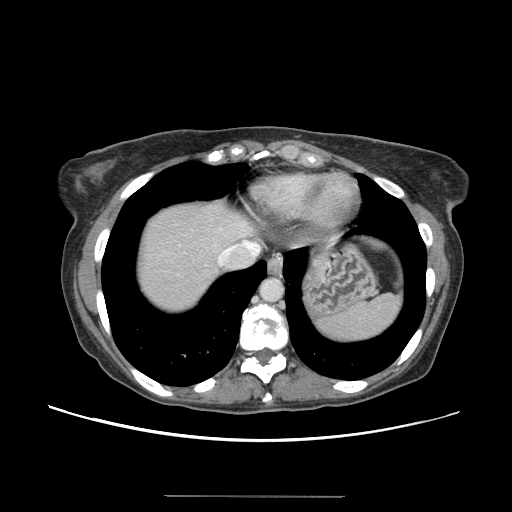
Contrast-enhanced abdominal CT, one axial slice. Position 129 of 144 along the scan axis. 120 kVp. Intravenous contrast given. Soft-tissue window (W 400 / L 40 HU). 512 × 512 image matrix. Female patient, age 53 years. From the clinical record (not read from this slice): diagnosis: colorectal cancer liver metastases, imaged before liver resection; multiple liver metastases: yes; largest metastasis: 1.1 cm; disease in both lobes: no.
Structures marked on this image (expert manual segmentation):
- hepatic veins: bounding box [x1, y1, x2, y2] px = [218, 241, 261, 265]
- liver: [135, 203, 252, 312]
- planned liver remnant (the part of the liver to remain after resection): [136, 200, 252, 291]